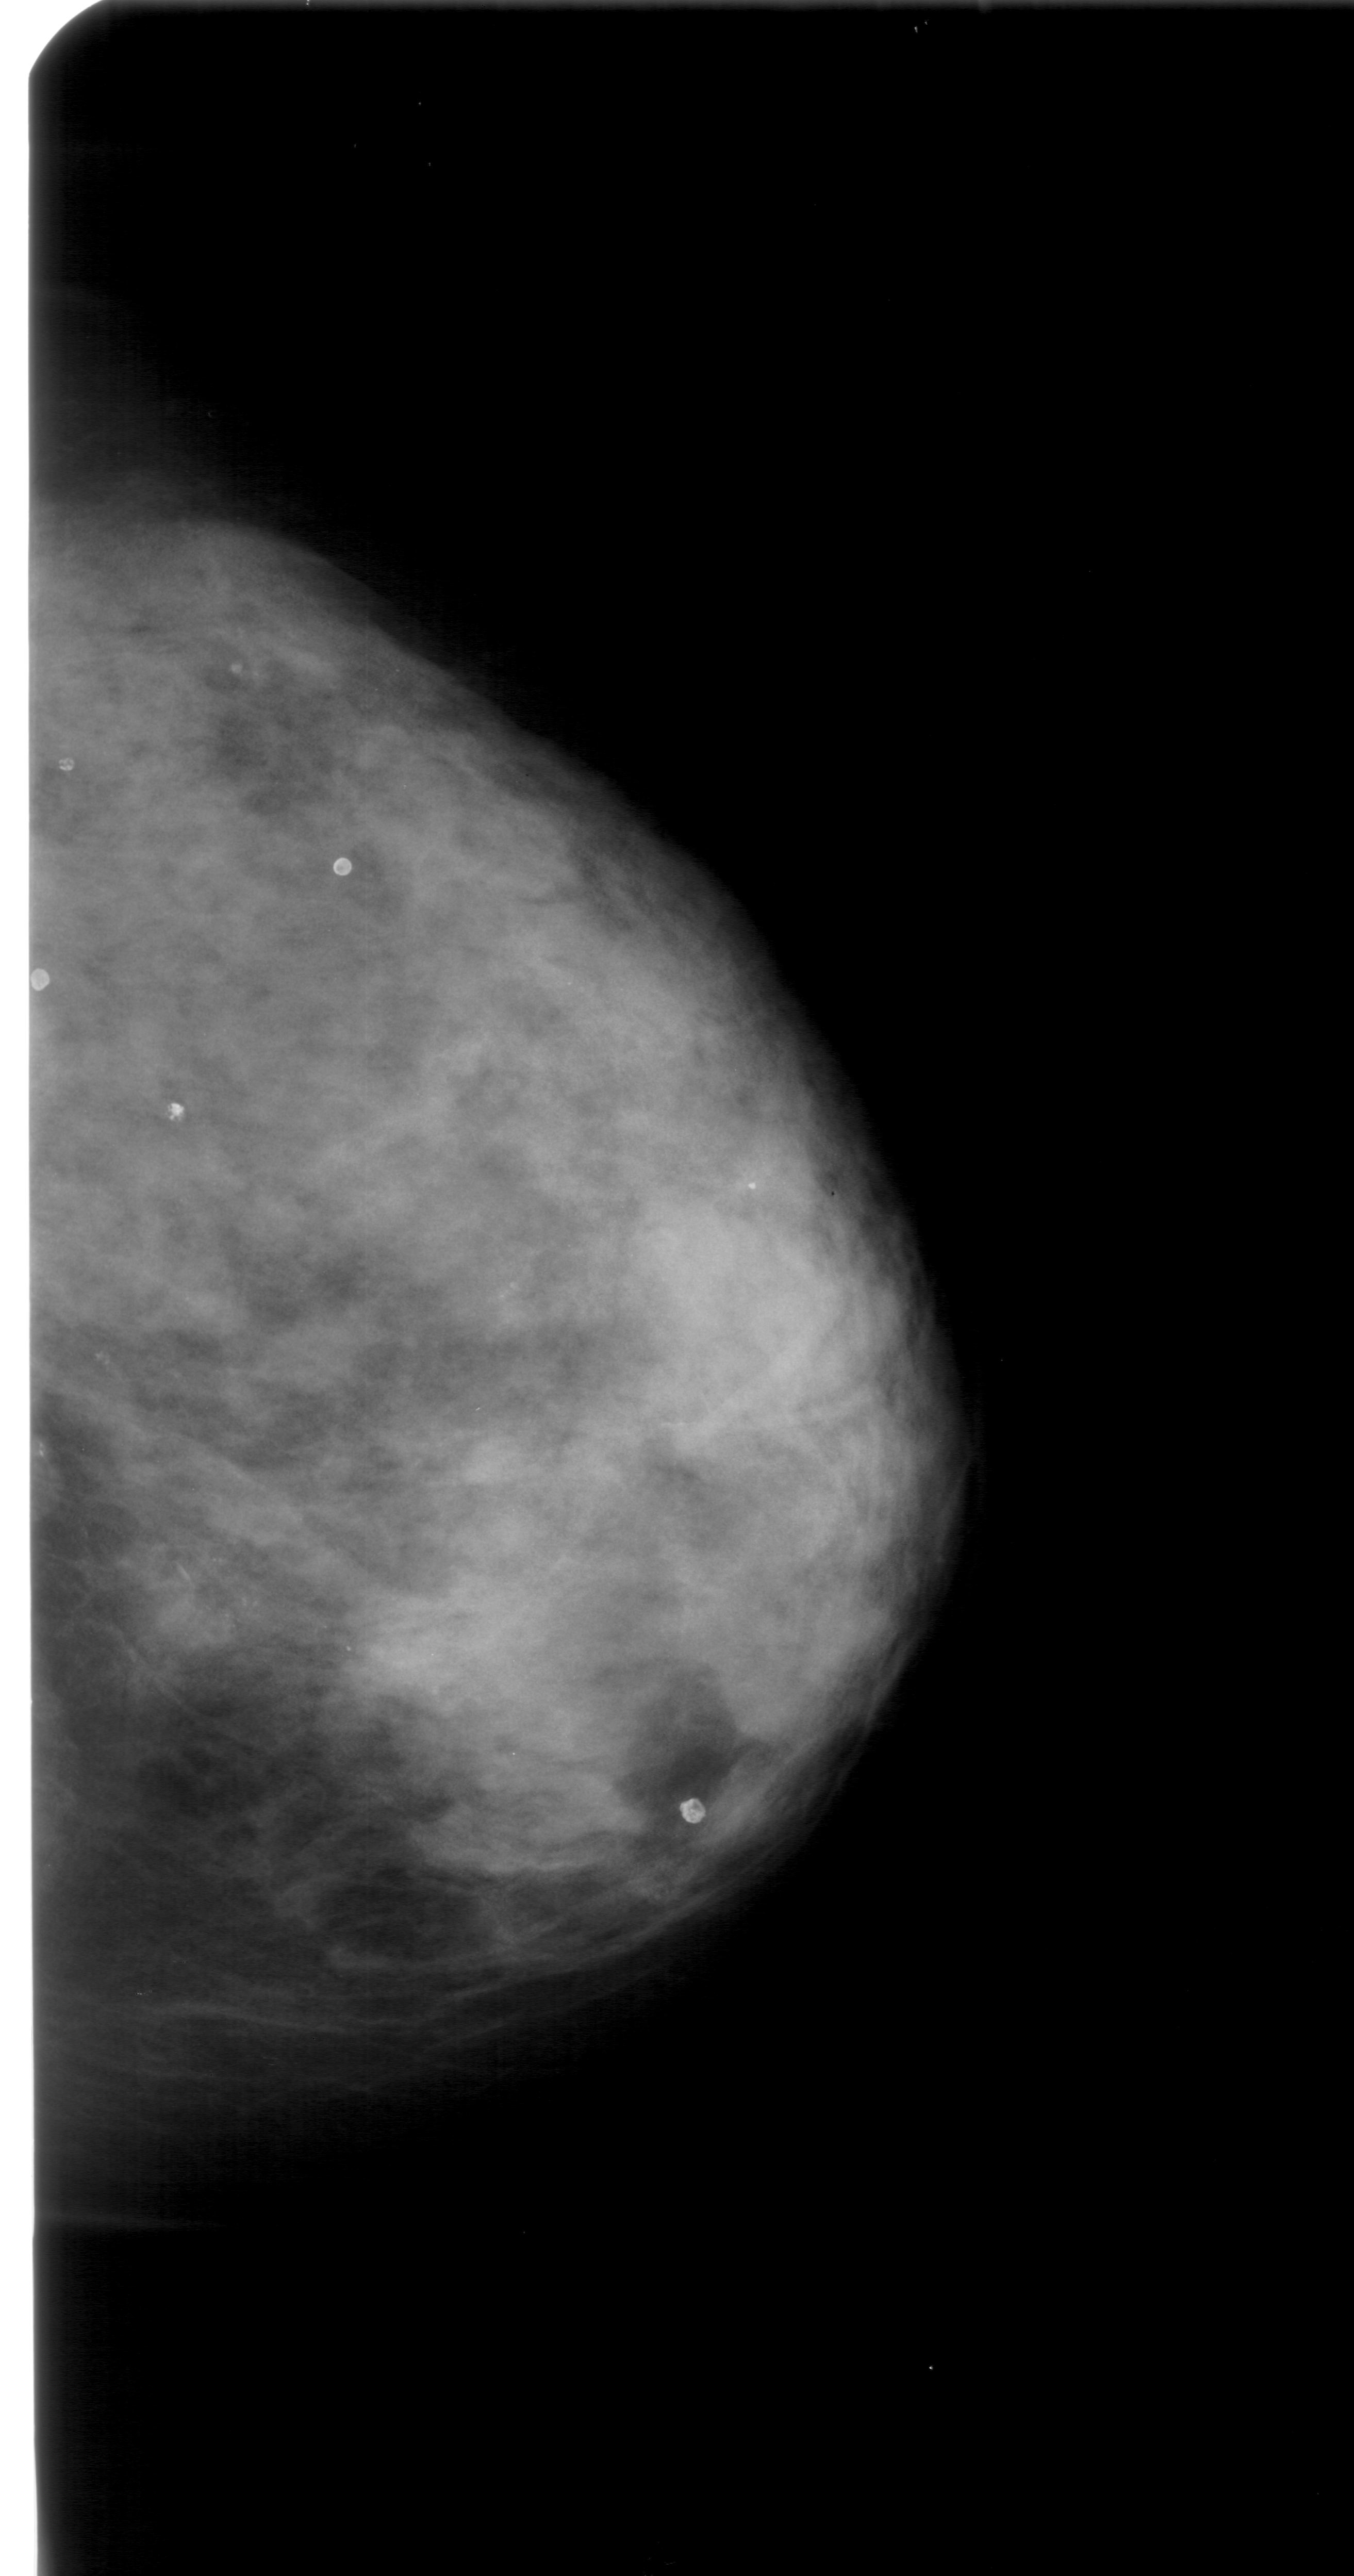
Scanned film-screen mammogram; right breast; CC view; BI-RADS breast density category 4 (scale 1–4); 1354 × 2576 image matrix.
Expert-marked regions of interest on this image (one box per marked abnormality):
- calcifications, morphology pleomorphic, distribution clustered; BI-RADS assessment category 4; subtlety rating 2 on a 1 (subtle) to 5 (obvious) scale; pathology (as recorded): benign: bounding box (x1, y1, x2, y2) in pixels: (138, 1524, 387, 1678)